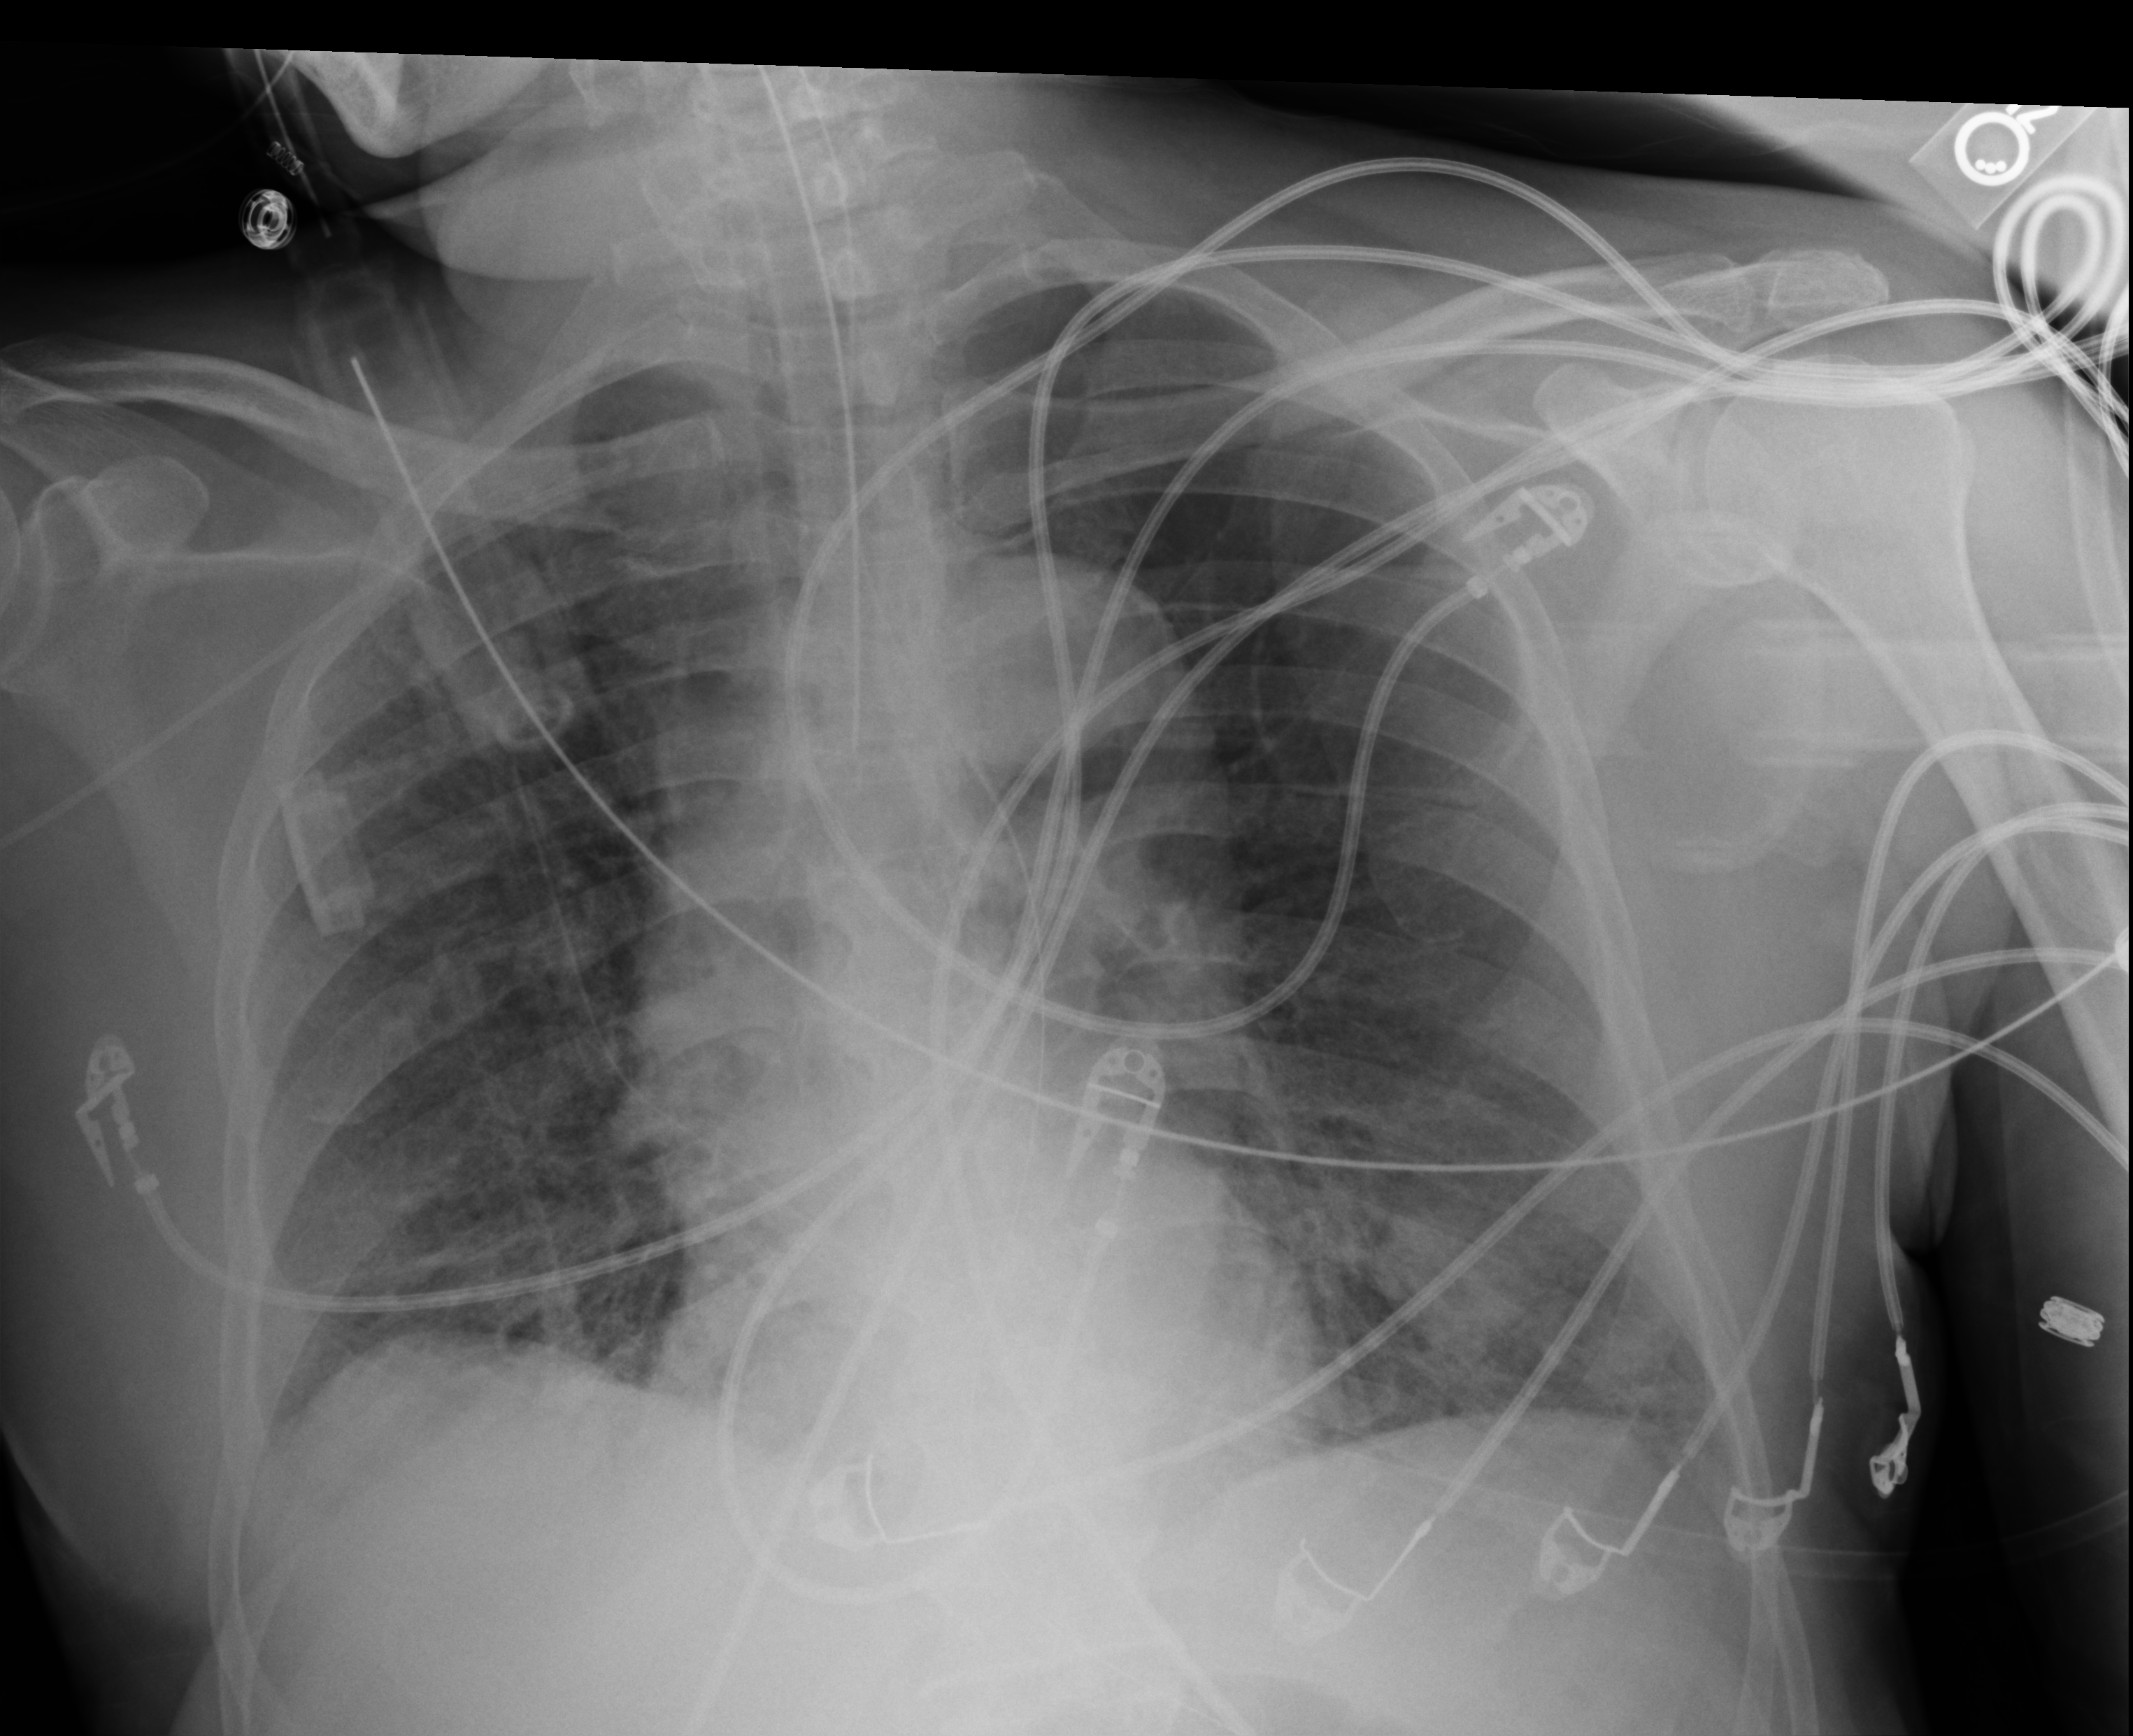
Chest X-ray (portable). Male patient hospitalised with COVID-19, age 60–74 years.
Hospital-stay facts (about this admission, not read from this image; timing relative to this image not recorded):
- length of hospital stay: 10 days
- admitted to intensive care during this hospital stay: yes